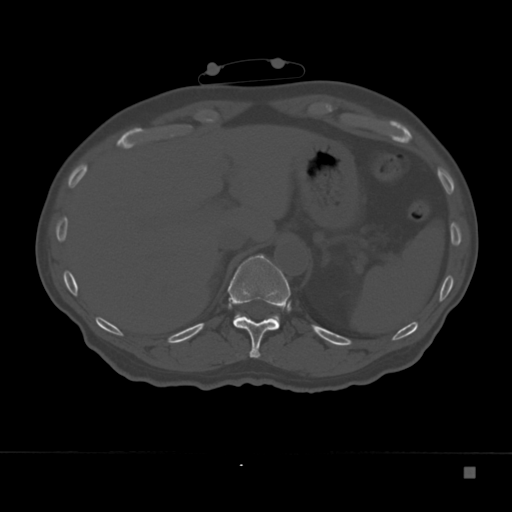
CT including the spine, one axial slice. Slice 149 of 332 in the series (ordered by position). Reconstruction kernel Br40s. 120 kVp. Bone window (W 1800 / L 400 HU). 512 × 512 image matrix, field of view 389 × 389 mm. Patient: male, 72 years. Case-level facts recorded for this patient, not image findings: primary cancer: skeletal.
Outlined on this slice (semi-automatically segmented with operator editing):
- T11 vertebra: bounding box <228,254,290,358> (left, top, right, bottom; pixels)
- T12 vertebra: <235,314,280,327>